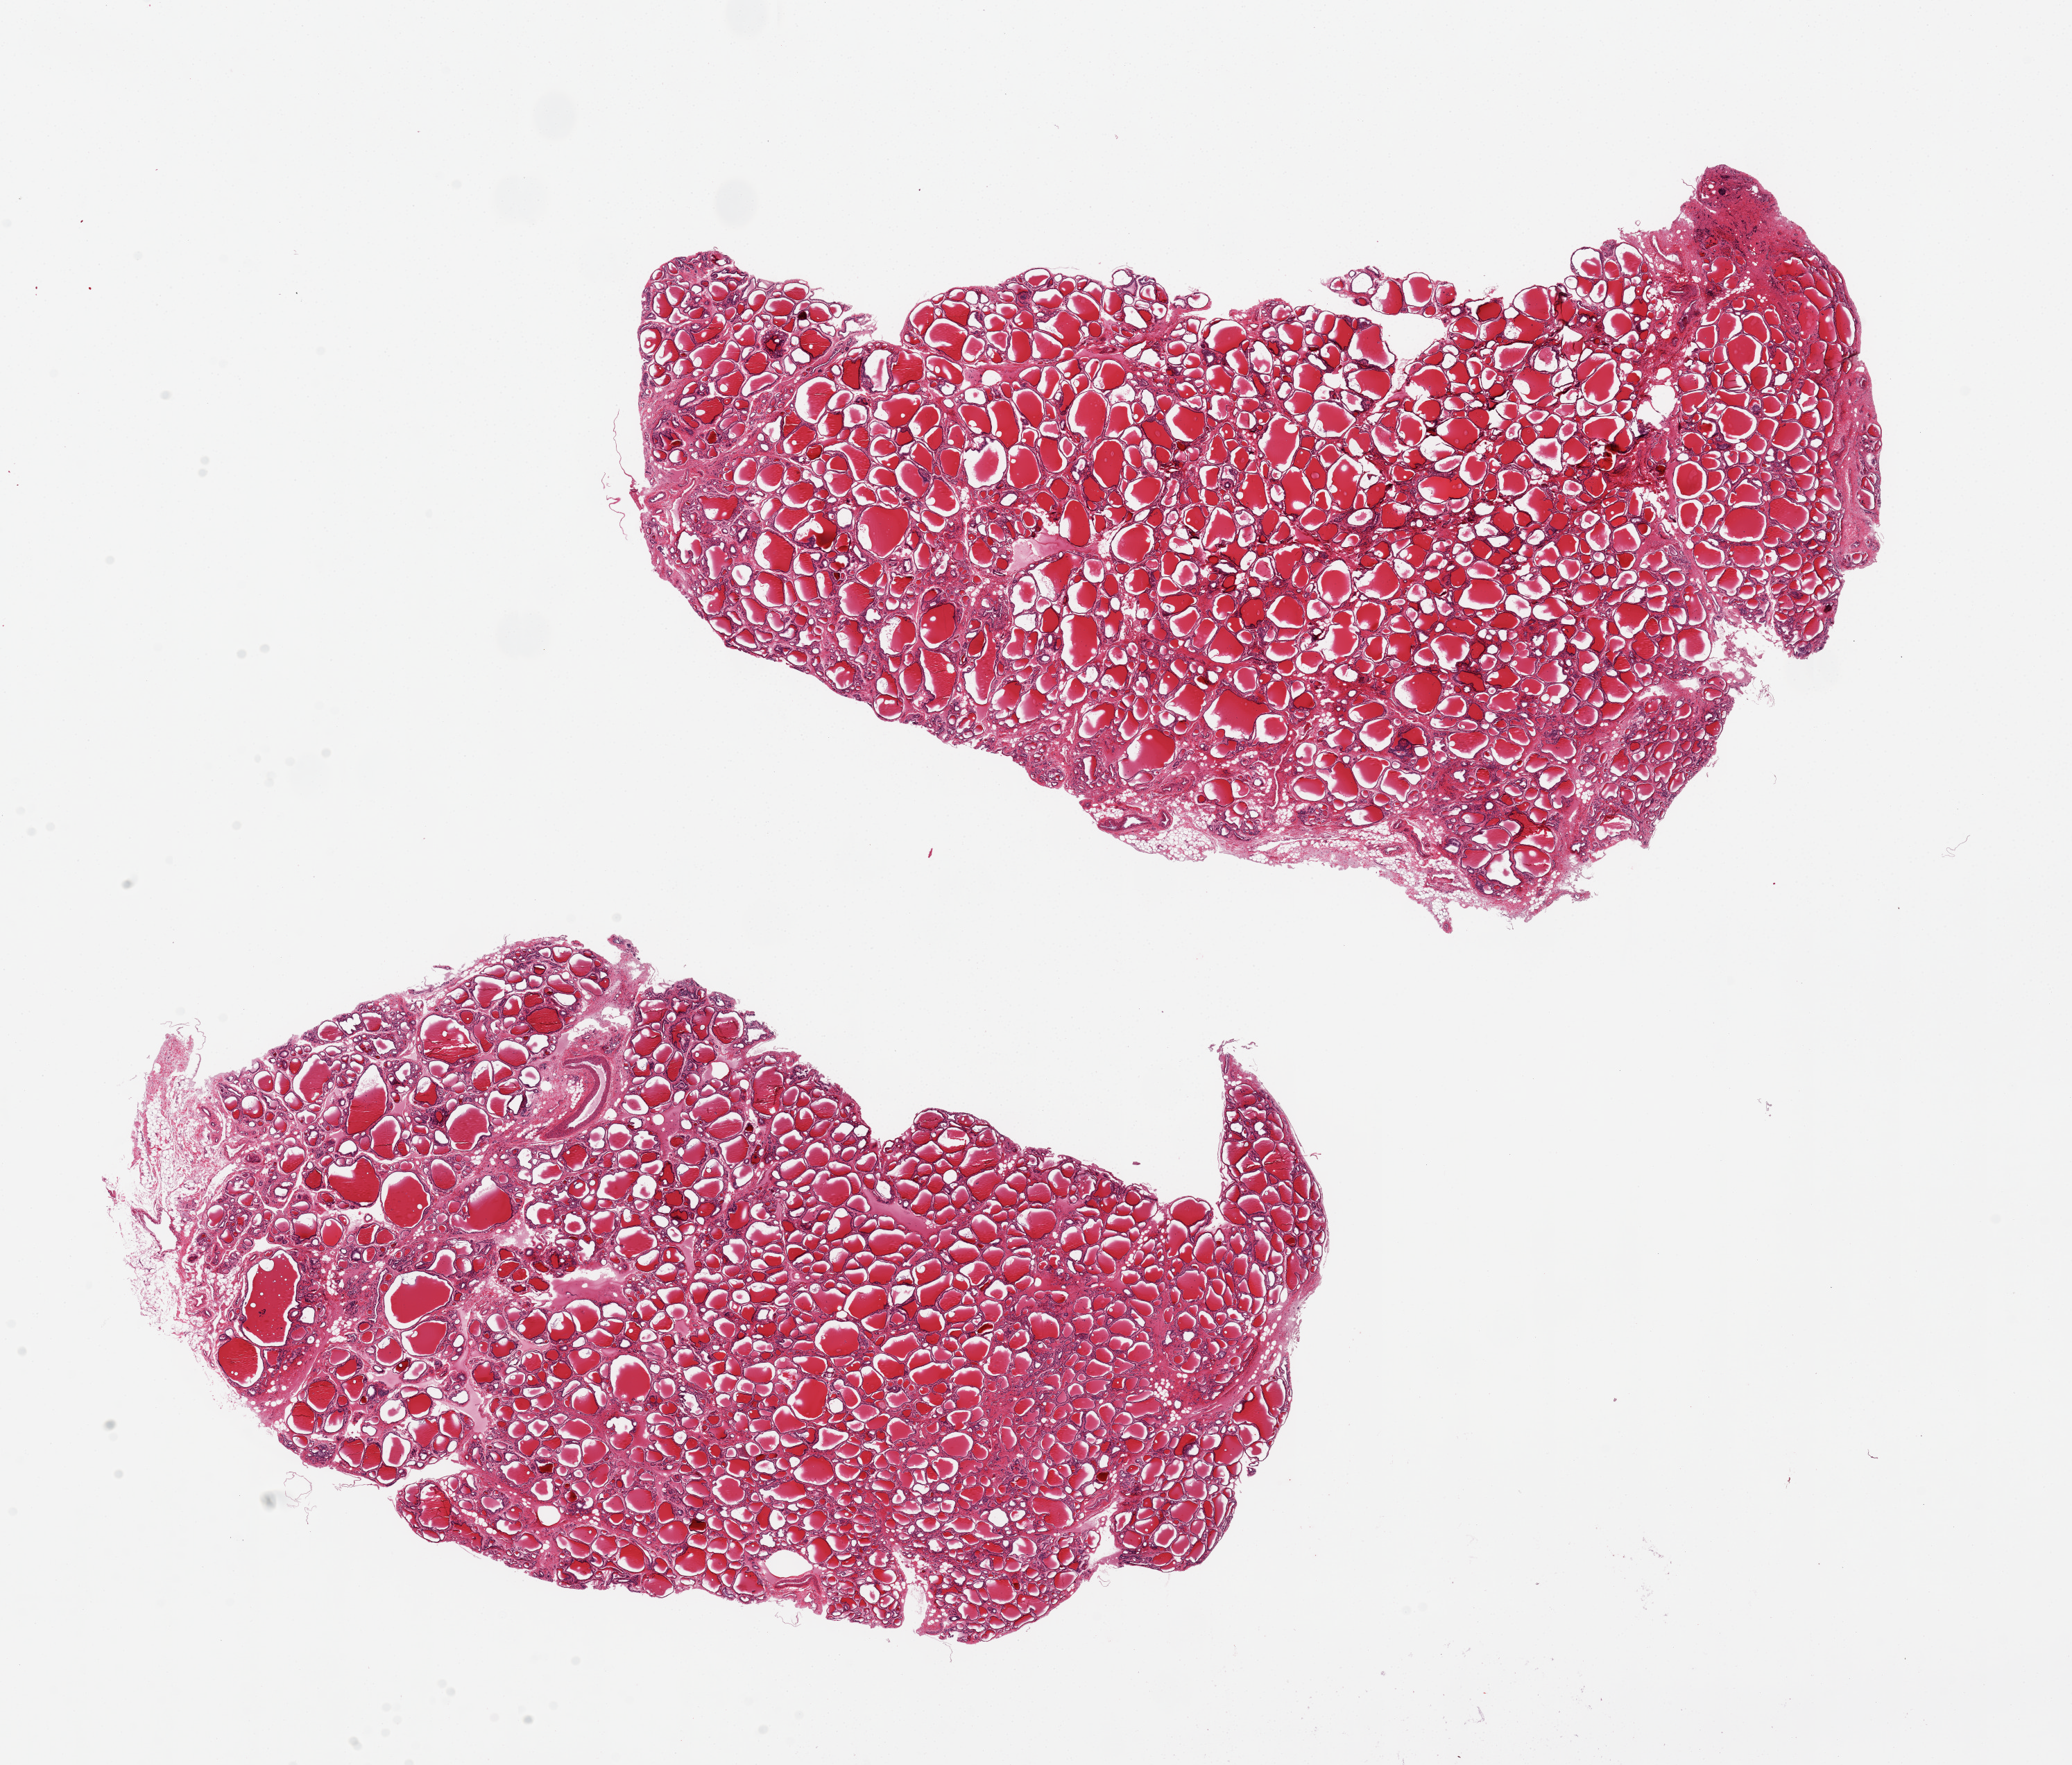
Whole-slide image, hematoxylin and eosin (H&E) stain, brightfield — shown as a low-resolution overview of the whole scanned area (about 23.6 x 20.1 mm, slide scanned at 20x). PAXgene-fixed paraffin-embedded (PFPE) section. Sampled site (target tissue): thyroid. Tissue donor sample. Male donor.
Pathologist's review note for this sample: 2 pieces, 13x9.5 and 13x7mm; mild regressive changes.